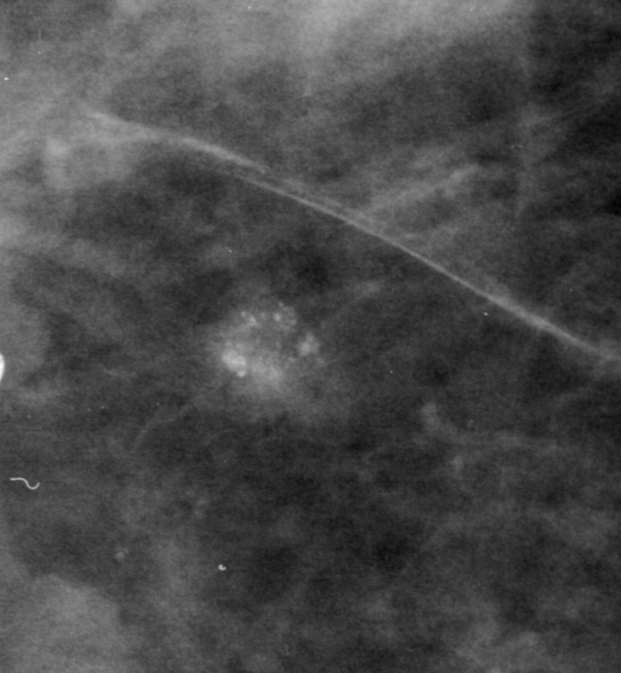
Region of interest cut from a scanned film mammogram (one marked finding), right breast, CC view.
- Calcifications, morphology amorphous, distribution clustered; BI-RADS assessment category 3; subtlety rating 3 on a 1 (subtle) to 5 (obvious) scale; pathology result (as recorded, not read from the image): malignant.